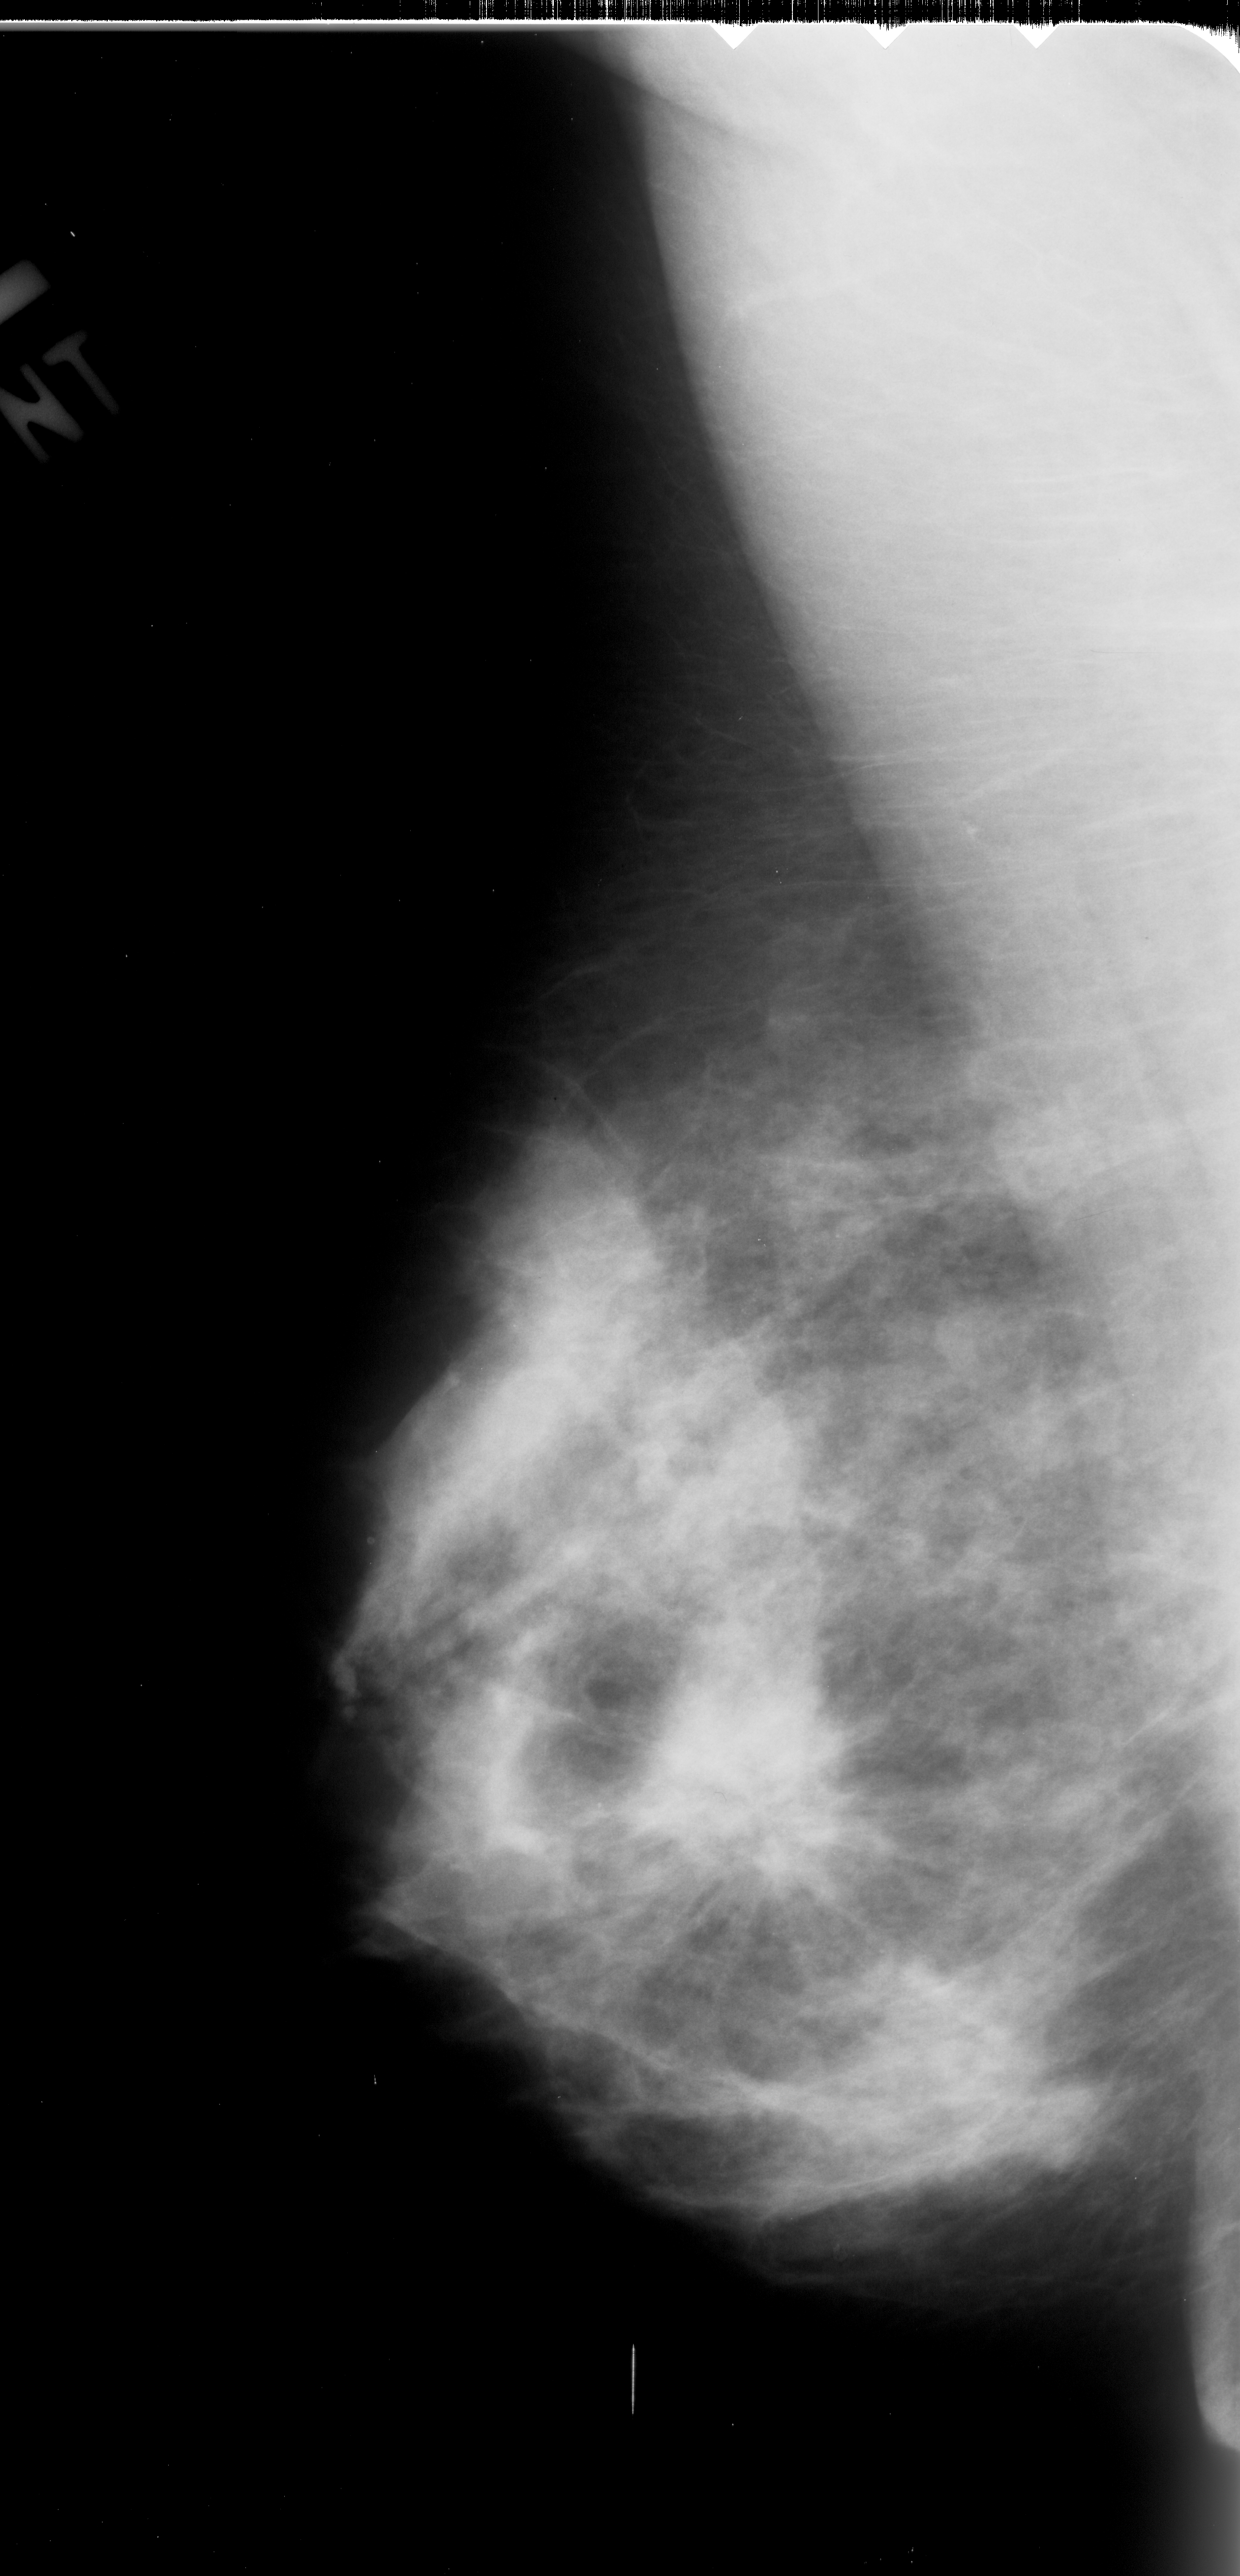
Digitized screen-film mammogram. Left breast. MLO view. 1240 × 2576 image matrix.
Expert-marked regions of interest on this image (one box per marked abnormality):
- mass, shape irregular, margins spiculated; BI-RADS assessment category 5; subtlety rating 5 on a 1 (subtle) to 5 (obvious) scale; pathology result (as recorded, not read from the image): malignant: bounding box [x1, y1, x2, y2] px = [607, 1658, 866, 1882]